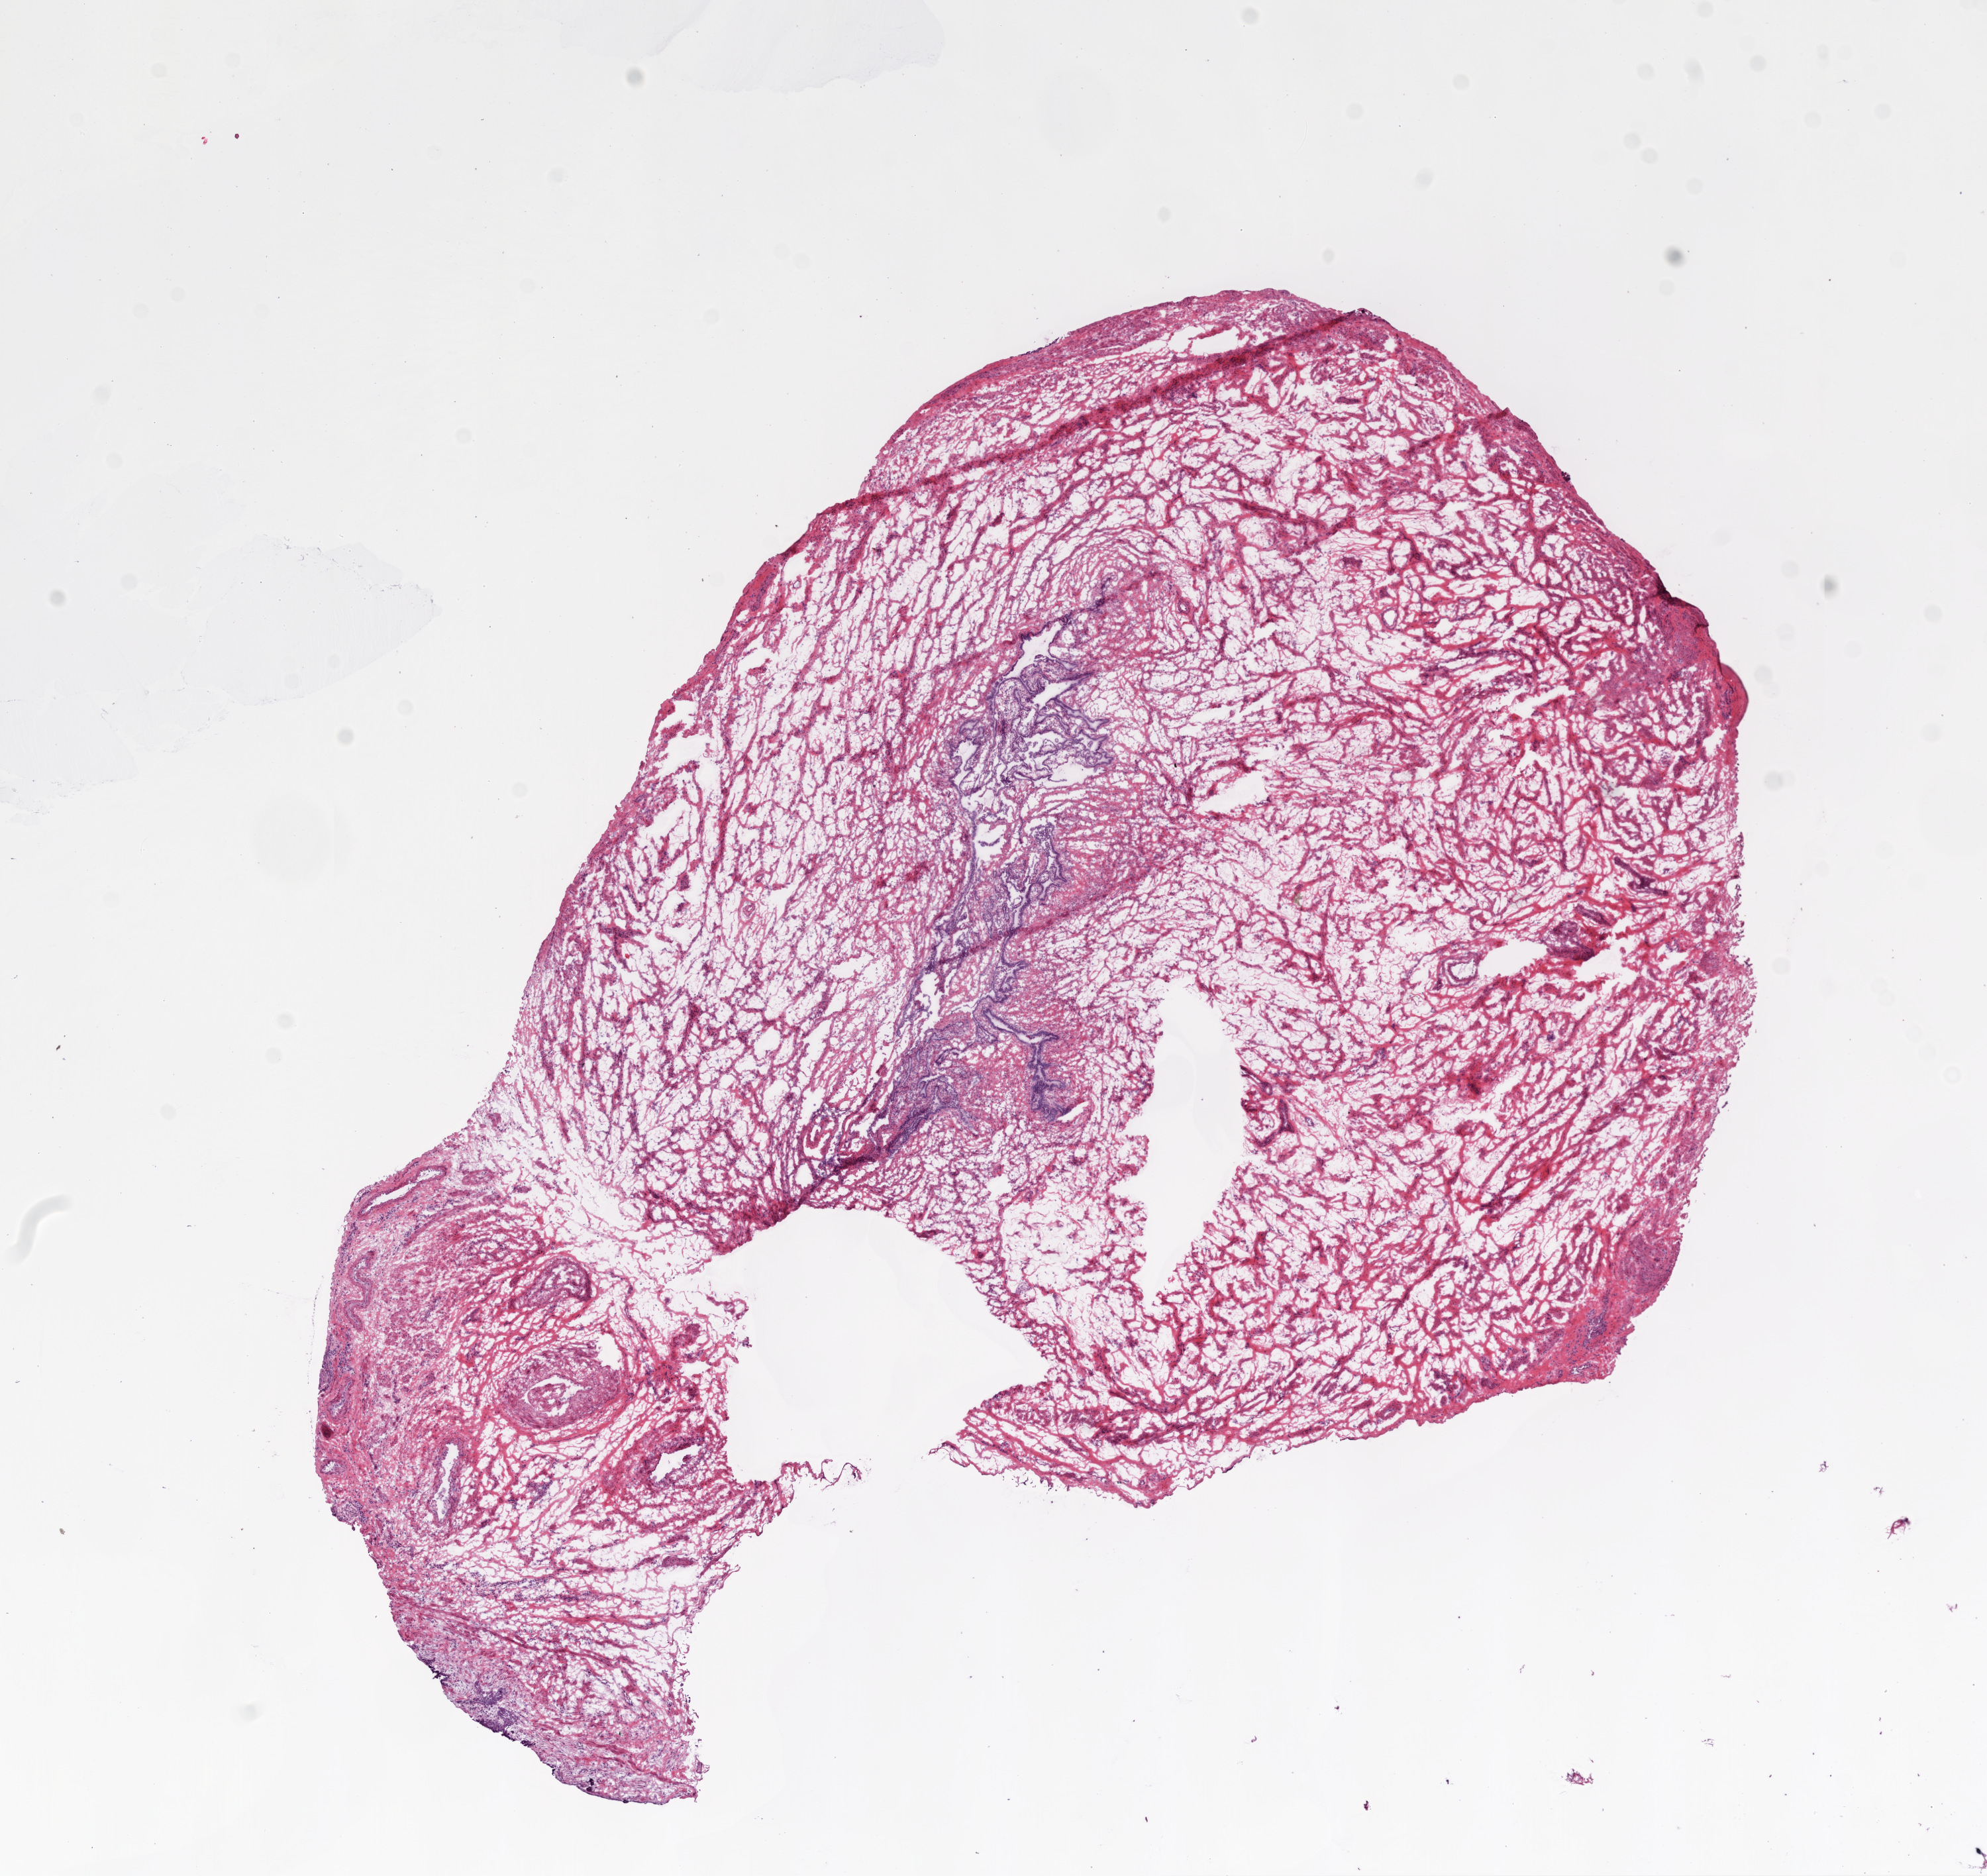
Hematoxylin and eosin (H&E) stained whole-slide image — shown as a low-resolution overview of the whole scanned area (about 12.0 x 11.4 mm, acquisition: 20x scan), frozen section, sample: solid tissue normal (non-tumour tissue), ovary. Female, age 55 years at initial diagnosis.
This section: solid tissue normal (non-tumour) sample from the same patient. Patient diagnosis: Serous cystadenocarcinoma, NOS.